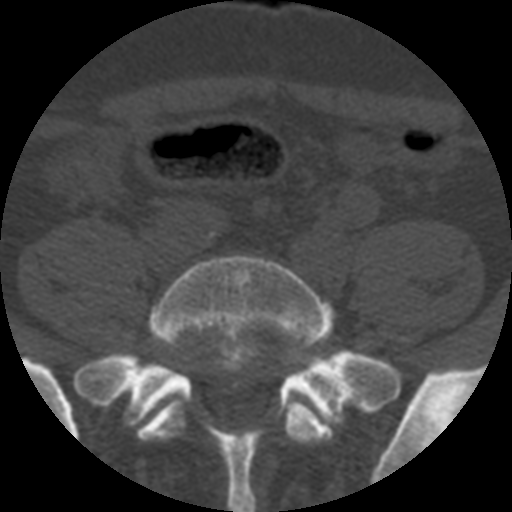
CT including the spine, one axial slice; slice 53 of 508 in the series (ordered by position); 120 kVp; bone window (W 1800 / L 400 HU); 1.25 mm slice thickness; 512 × 512 image matrix, field of view 160 × 160 mm. Patient age 57 years. From the clinical record (not read from this slice): primary cancer: prostate.
Outlined on this slice (semi-automatic segmentation, software-assisted and operator-edited):
- L5 vertebra: bounding box <137,255,334,444> (left, top, right, bottom; pixels)